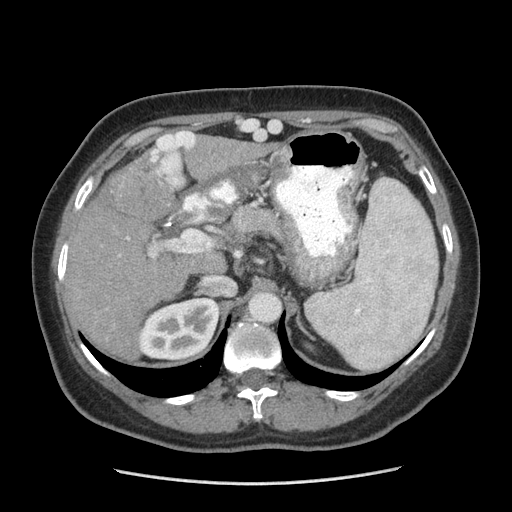
Contrast-enhanced abdominal CT (liver protocol), one axial slice. Slice 153 of 185 in the series (ordered by position). Soft-tissue window (W 400 / L 40 HU). 512 × 512 image matrix. Case-level facts recorded for this patient, not image findings: diagnosis: hepatocellular carcinoma (patient treated with transarterial chemoembolisation; whether this scan precedes or follows treatment is not stated here); TNM stage (as recorded): Stage-I; Child-Pugh class: A; tumour differentiation: poorly differentiated; tumour nodularity: uninodular.
Outlined on this slice (semi-automatic segmentation, software-assisted and operator-edited):
- liver parenchyma outside the tumour (the mass and vessels are separate outlines, so this box may not span the whole liver): bounding box <62,130,251,354> (left, top, right, bottom; pixels)
- mass: <108,163,171,221>
- liver vessels: <64,131,213,257>